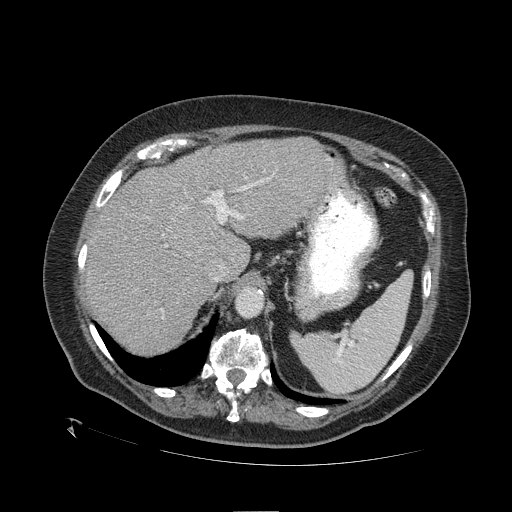
Contrast-enhanced abdominal CT (liver protocol), one axial slice; slice 78 of 109 in the series (ordered by position); reconstruction kernel STANDARD; one of 2 acquisitions stored at this slice position; soft-tissue window (W 400 / L 40 HU); 2.5 mm slice thickness; 512 × 512 image matrix, field of view 460 × 460 mm. From the clinical record (not read from this slice): diagnosis: hepatocellular carcinoma (patient treated with transarterial chemoembolisation; whether this scan precedes or follows treatment is not stated here); TNM stage (as recorded): Stage-I; Child-Pugh class: A; tumour differentiation: no biopsy; tumour nodularity: uninodular.
Annotated regions visible in this slice (semi-automatic segmentation, software-assisted and operator-edited):
- liver parenchyma outside the tumour (the mass and vessels are separate outlines, so this box may not span the whole liver): box from (x=84, y=136) to (x=346, y=353) px
- mass: (x=166, y=202)–(x=214, y=257)
- liver vessels: (x=105, y=177)–(x=329, y=311)